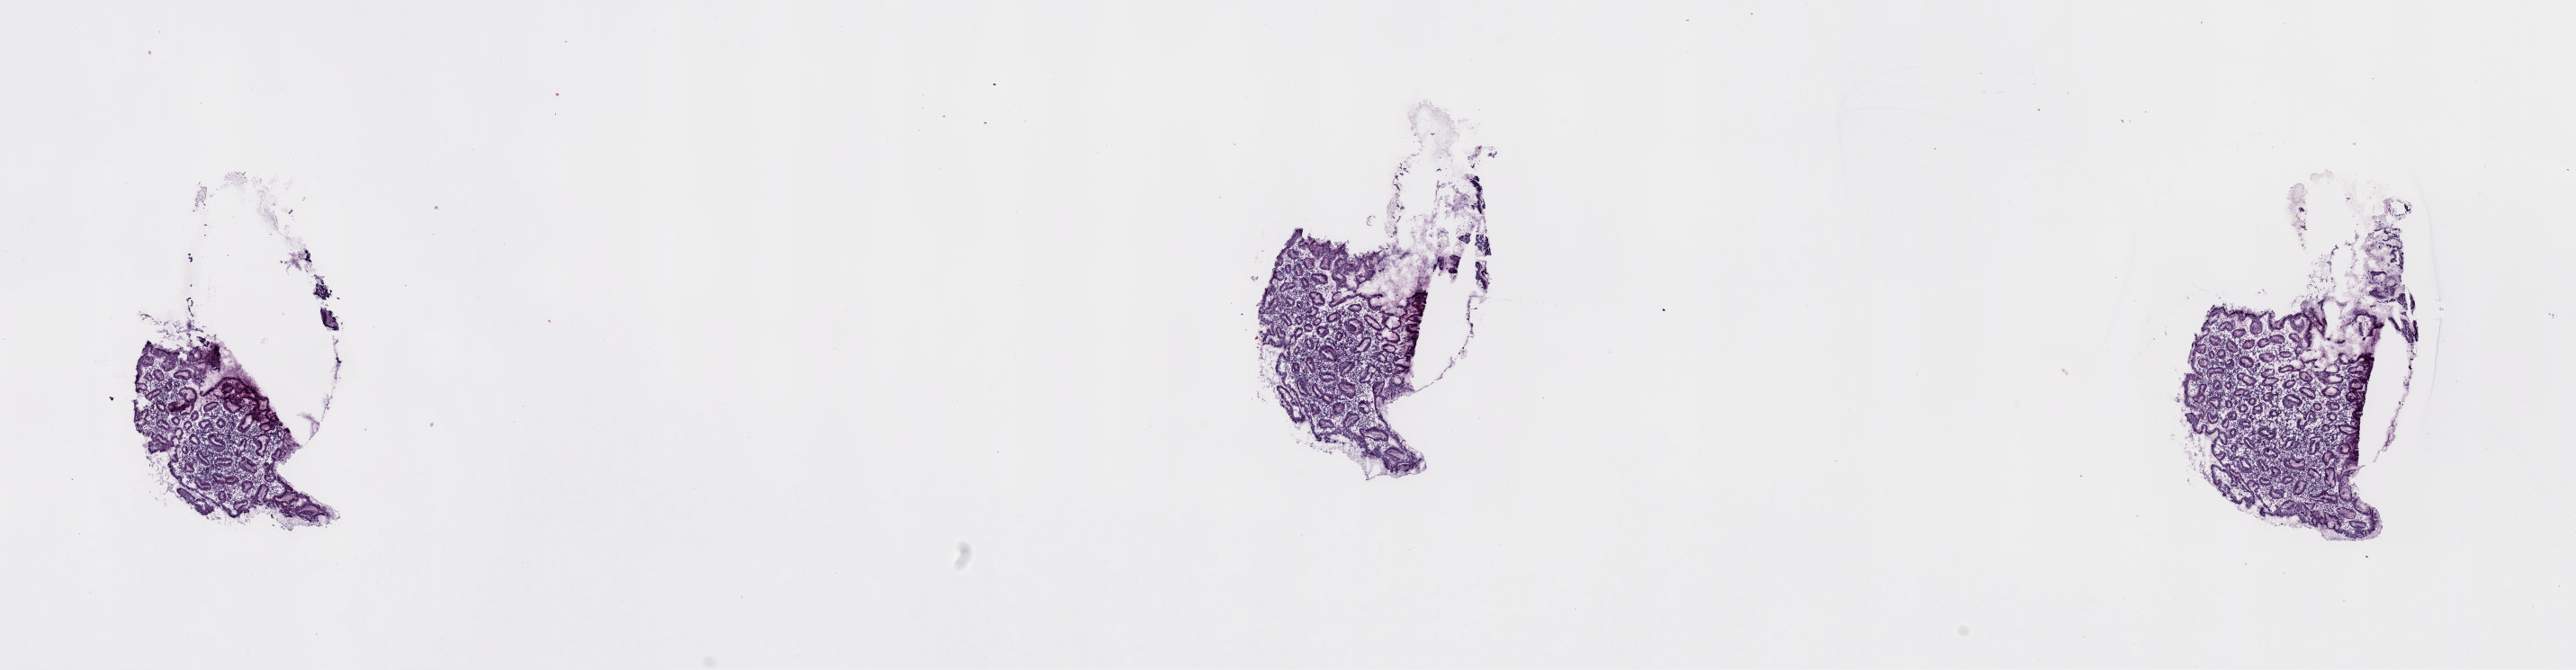
Whole-slide histology image, Hematoxylin and eosin (H&E) stained — a low-resolution overview of the entire scanned area, about 22.6 x 5.9 mm (acquisition: 20x scan), frozen section from the top of the tissue portion, solid tissue normal (non-tumour tissue) sample from the stomach. Patient: male, age at initial diagnosis 71 years. Composition of this section per pathologist review: tumour cells 0%, tumour nuclei 0%, normal cells 60%, stromal cells 40%, necrosis 0%. Infiltration values recorded for this section: lymphocyte infiltration 10%, monocyte infiltration 3%, neutrophil infiltration 0%.
* this section: solid tissue normal (non-tumour) sample from the same patient
* patient diagnosis: Papillary adenocarcinoma, NOS (fundus of stomach)